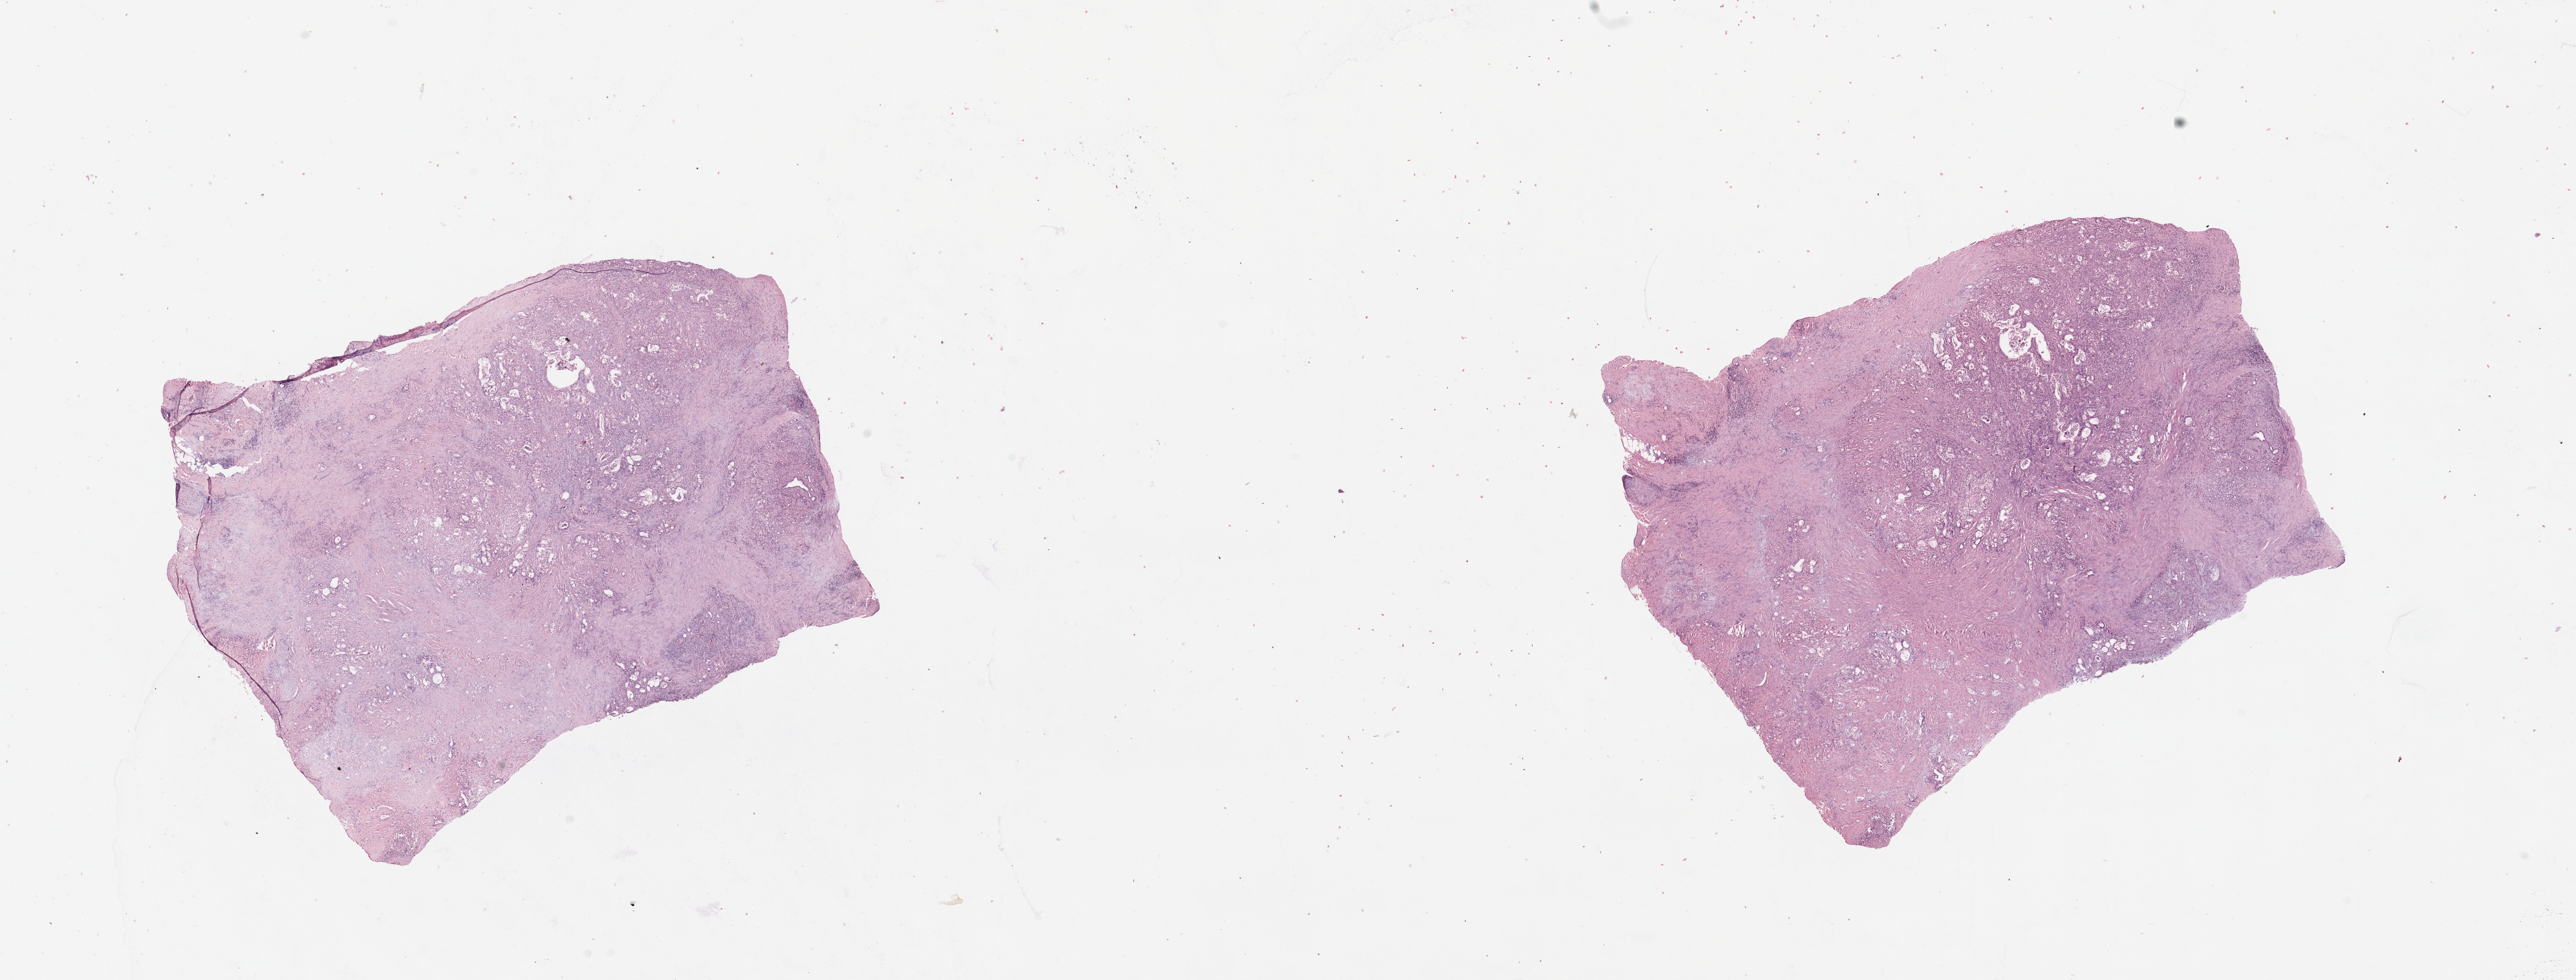
Digitized Hematoxylin and eosin (H&E) stained tissue section (whole slide) — whole scanned area (about 31.5 x 12.0 mm) shown as a low-resolution overview. Pancreas, tissue type not recorded.
• patient diagnosis (cohort enrolment): ductal adenocarcinoma (pancreas)